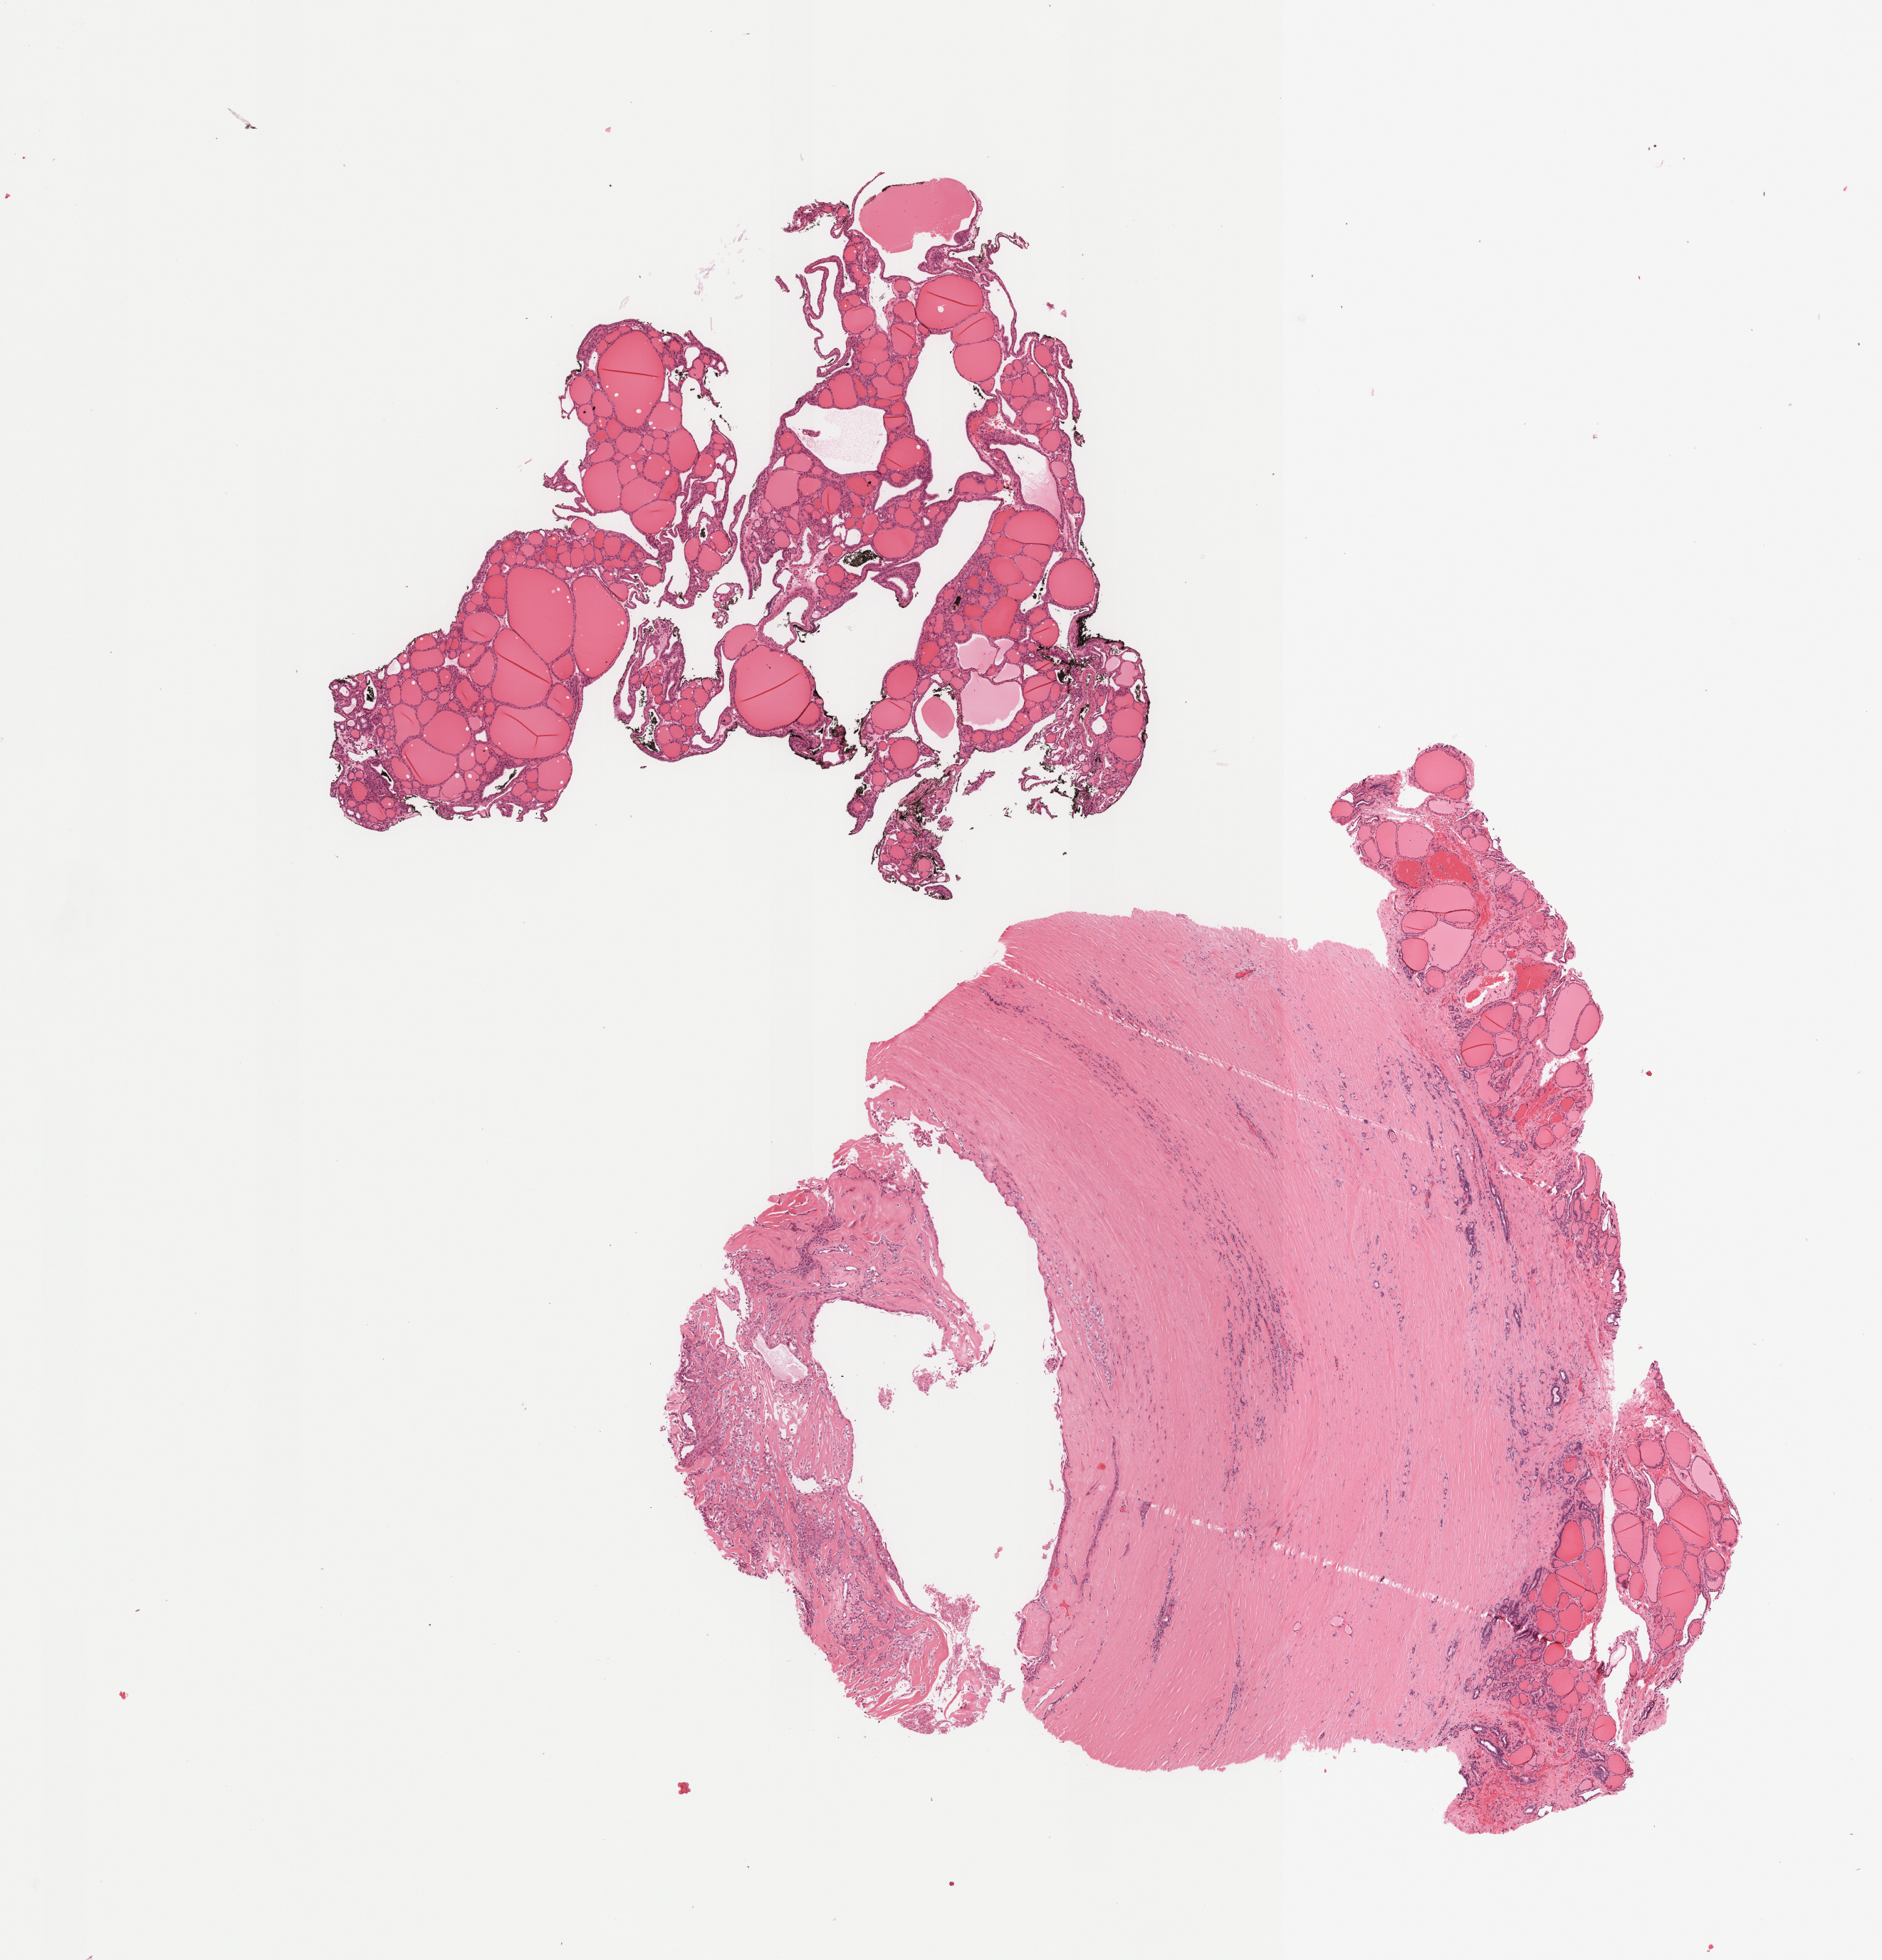
Whole-slide histology image, H&E, low-resolution overview of the scanned area, about 10.6 x 11.1 mm; formalin-fixed paraffin-embedded (FFPE) diagnostic section; thyroid, primary tumour sample. Patient: female, age at initial diagnosis 40 years.
Lymph nodes positive (case pathology): 1 of 3 examined. Pathologic diagnosis: Papillary carcinoma, follicular variant (thyroid gland). Laterality: left. AJCC pathologic stage: I (7th edition).